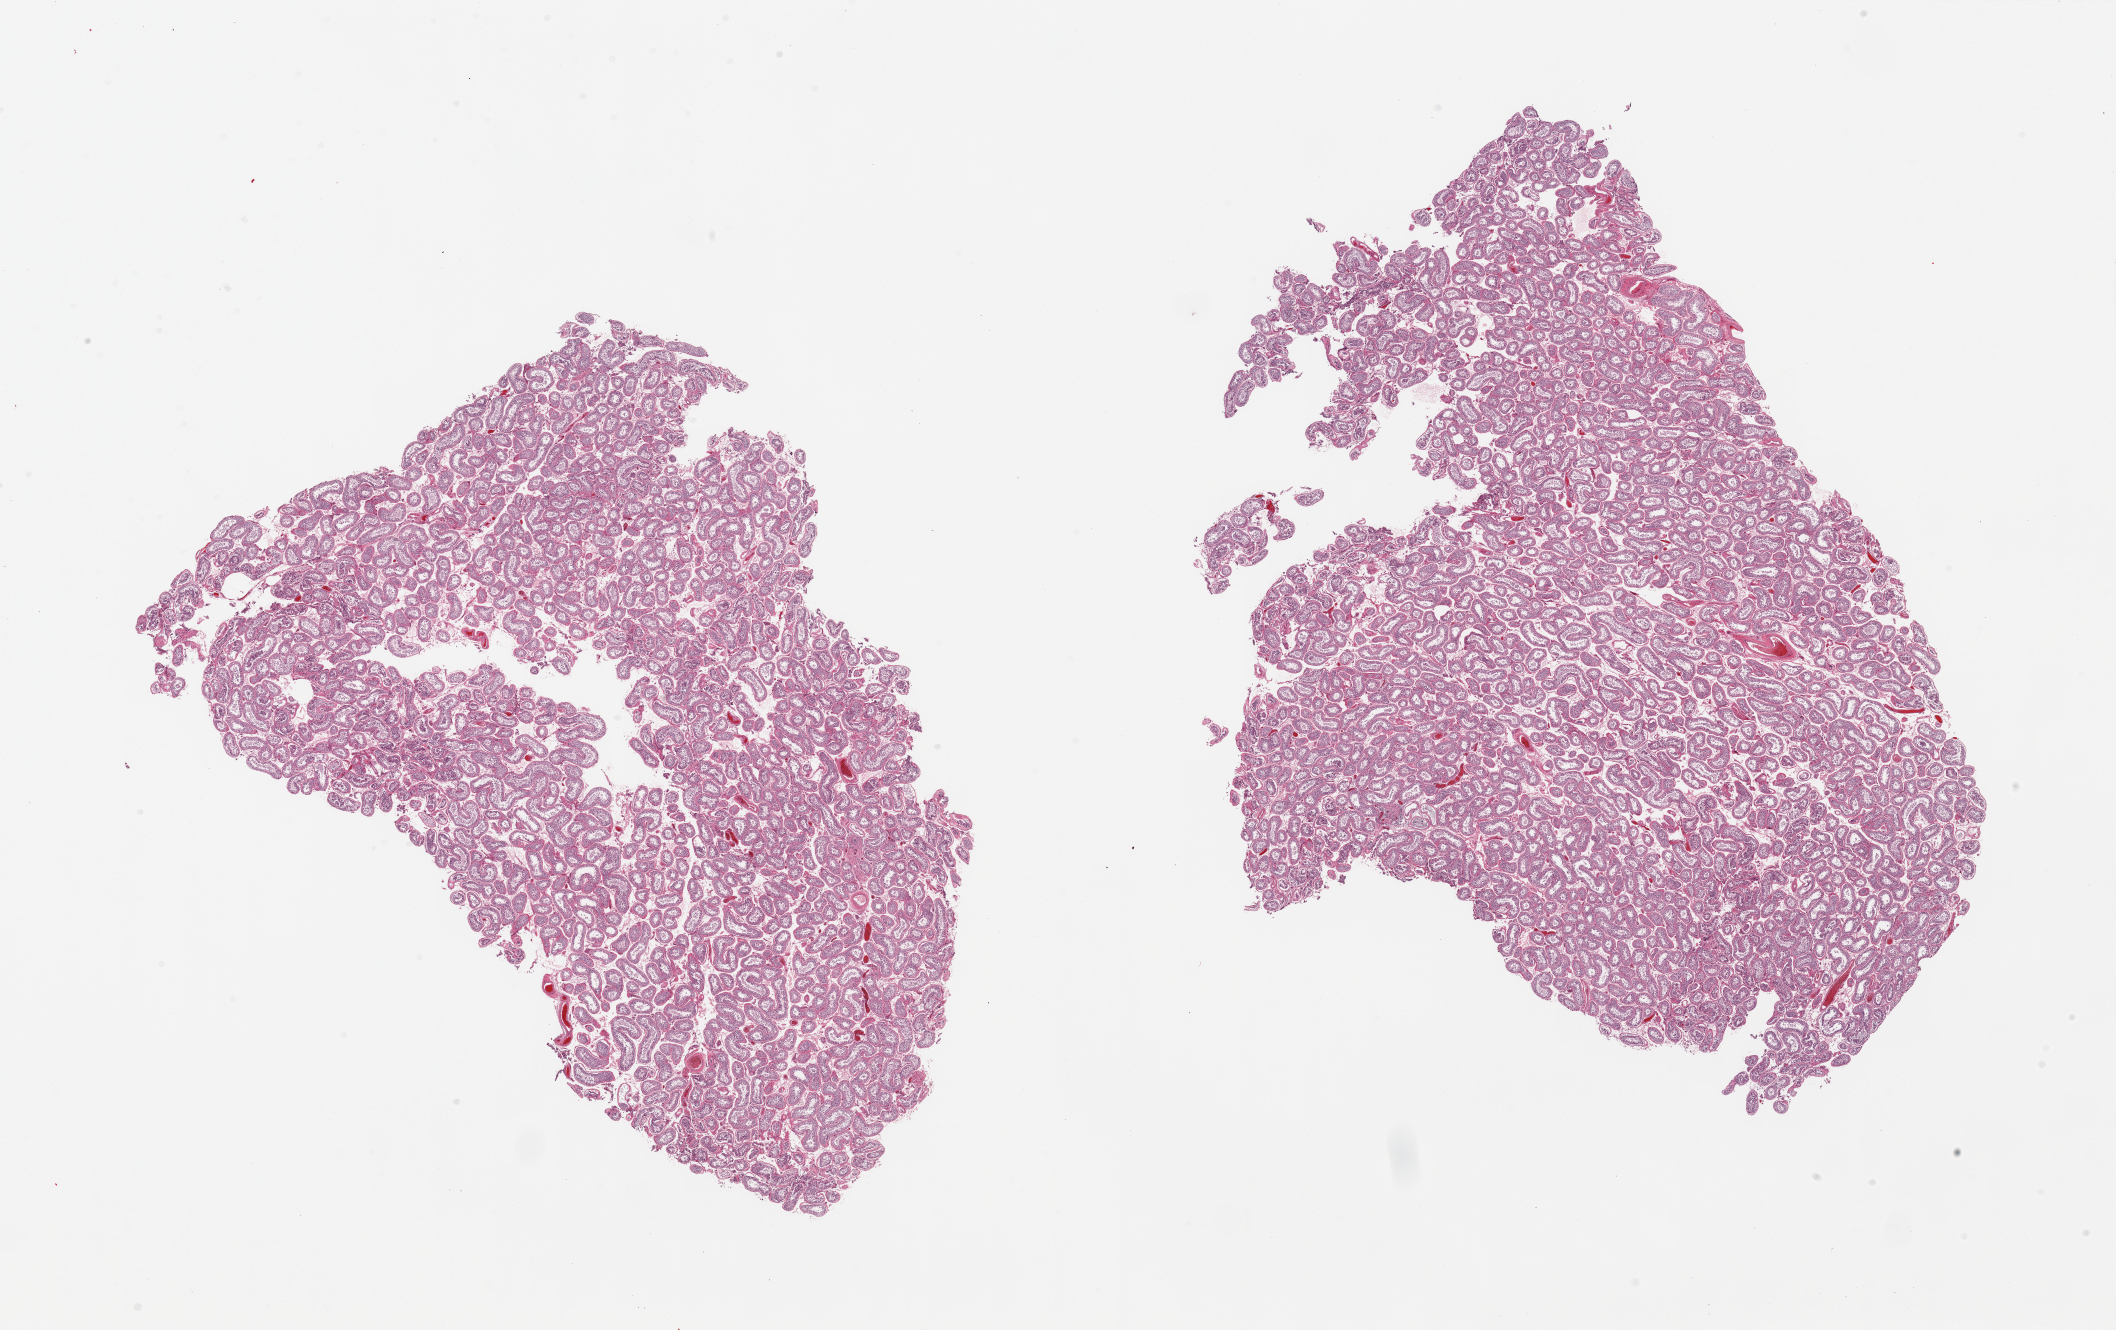
Digitized haematoxylin and eosin-stained section, shown as a low-resolution overview of the whole scanned area (about 33.5 x 21.0 mm, acquisition: 20x scan), PAXgene-fixed paraffin-embedded (PFPE) section, target tissue: testis, tissue donor sample. Donor sex: male.
Reviewer comment on this tissue sample: 2 pieces; spermatogenesis.